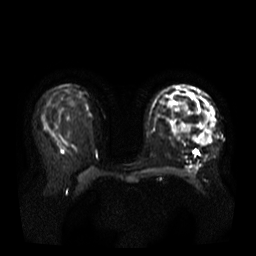
Breast MRI, one axial slice. Slice 21 of 37 in the series (ordered by position). Diffusion-weighted series; image 2 of 4 stored at this slice position (different b-values; order by instance number). 3 T. 5 mm slice thickness. 256 × 256 image matrix. Female patient.
Structures marked on this image (expert manual segmentation):
- tumour on diffusion-weighted imaging: box from (x=193, y=103) to (x=215, y=145) px